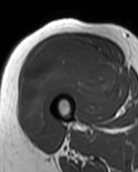
MRI of an extremity soft-tissue mass, one axial slice. Slice 42 of 99 in the series (ordered by position). MR volume resampled by the dataset authors to the PET/CT grid (not the native acquisition matrix). 3.27 mm slice thickness. 138 × 172 image matrix, field of view 135 × 168 mm. Female patient. Case-level facts recorded for this patient, not image findings: histological type: pleiomorphic undifferentiated sarcoma; grade: high; site of the primary tumour: right quadricep.
Annotated regions visible in this slice (expert contour drawn on MRI and transferred to this co-registered scan by the dataset authors):
- gross tumour volume including surrounding oedema: bounding box [x1, y1, x2, y2] px = [21, 38, 120, 131]
- gross tumour volume (mass): [21, 38, 120, 131]